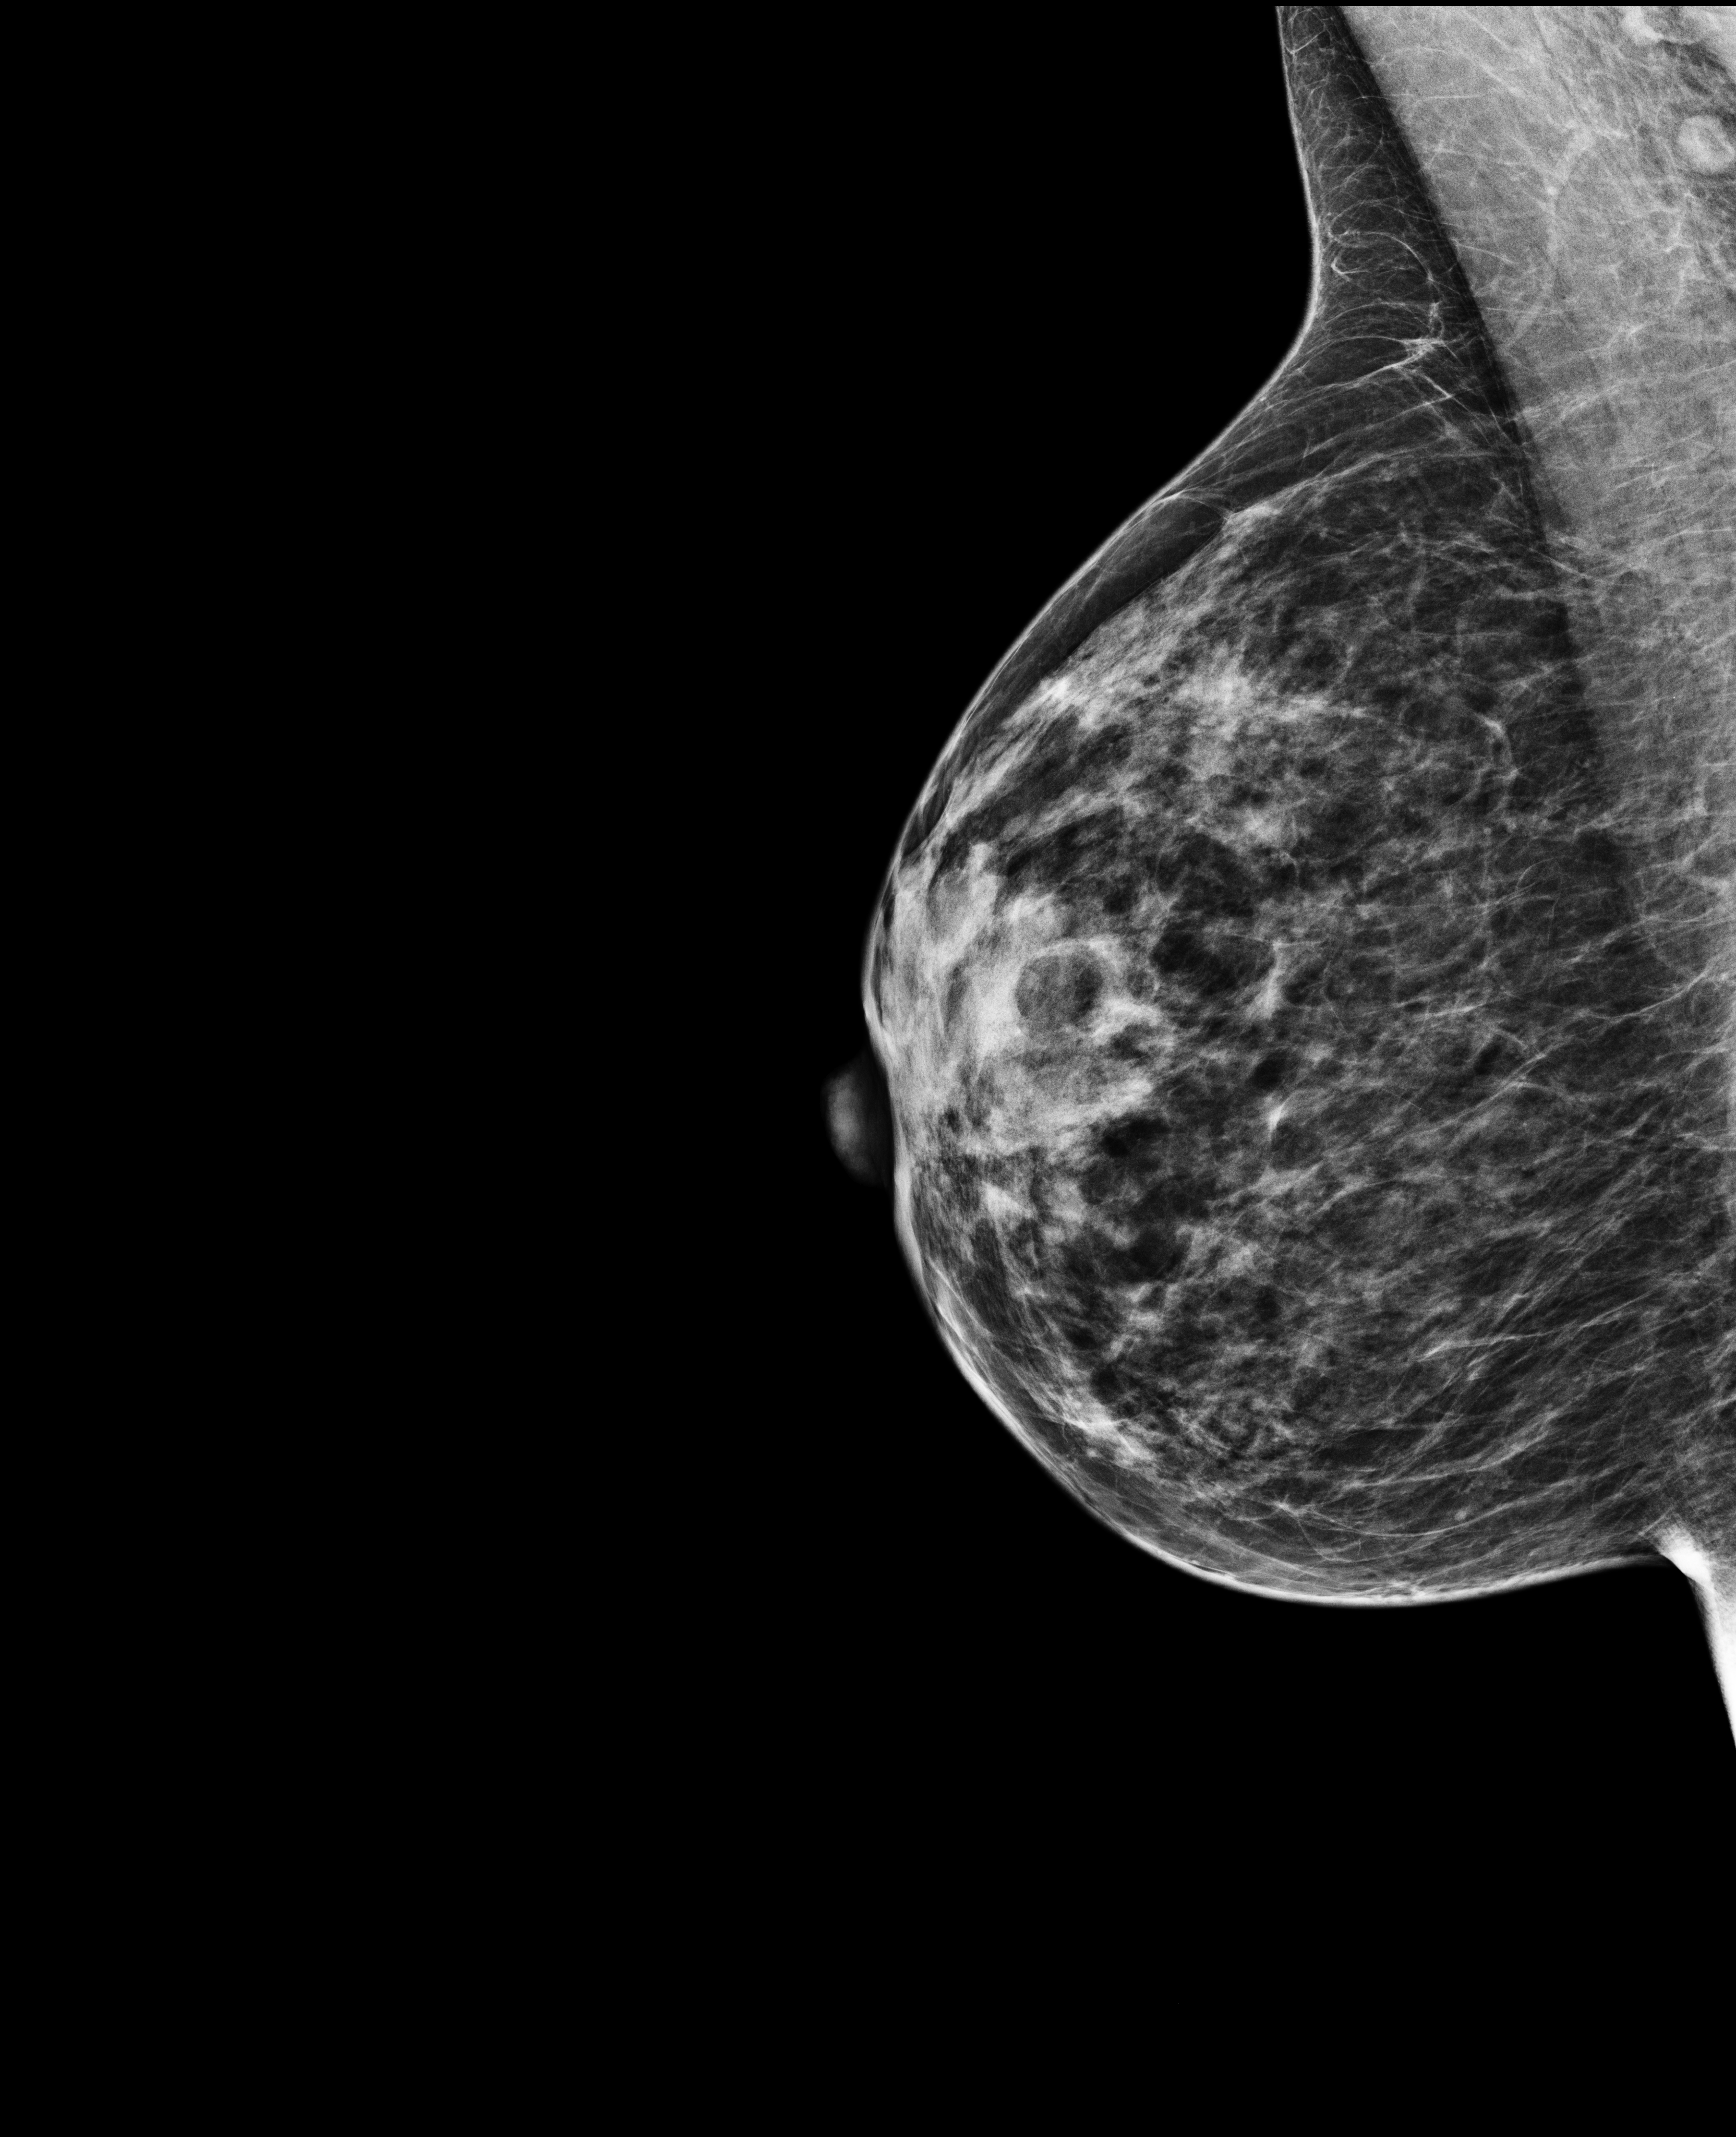
Annual screening mammography examination, compressed breast thickness 38 mm, system: Selenia Dimensions. Patient: female, 51 years.
Image type: full-field digital mammogram. Breast: right. Projection: MLO view.